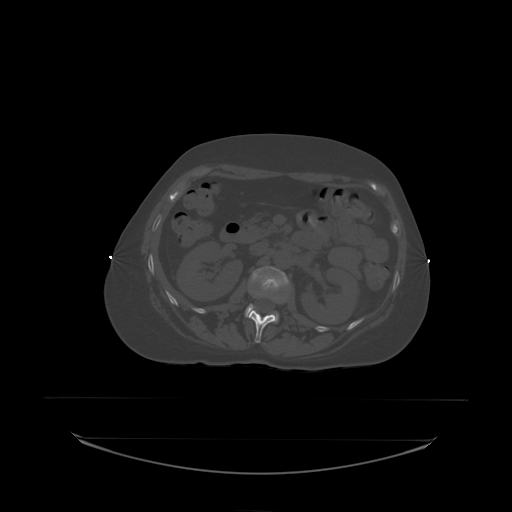
CT including the spine, one axial slice. Position 79 of 242 along the scan axis. Bone window (W 1800 / L 400 HU). 2.5 mm slice thickness. 512 × 512 image matrix, field of view 500 × 500 mm. Patient: female, 53 years. Case-level facts recorded for this patient, not image findings: primary cancer: lung; vertebrae with lytic lesions (as recorded): T7, L1.
Outlined on this slice (semi-automatically segmented with operator editing):
- L1 vertebra: box from (x=249, y=309) to (x=275, y=338) px
- L2 vertebra: (x=245, y=267)–(x=289, y=324)